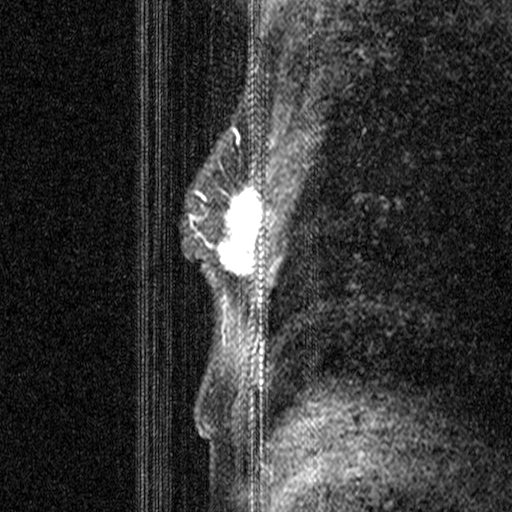
Breast MRI (dynamic contrast-enhanced), one sagittal slice. Dynamic contrast-enhanced study with each time point stored as its own series, time point 2 of 3 at this slice position (early post-contrast, ordered by acquisition time). 1.5 T. TE 4.5 ms, TR 11 ms. 512 × 512 image matrix, field of view 200 × 200 mm. Patient: female, 44 years. From the clinical record (not read from this slice): setting: breast cancer imaged before/during neoadjuvant chemotherapy; receptor status: HR-positive, HER2-negative.
Outlined on this slice (semi-automatically segmented with operator editing):
- analysis volume of interest (the breast-tissue region the enhancement analysis was run in; not a lesion): box from (x=206, y=164) to (x=258, y=299) px
- tumour enhancement mask (voxels above the 90 % enhancement threshold inside the analysis volume of interest): (x=217, y=164)–(x=258, y=274)